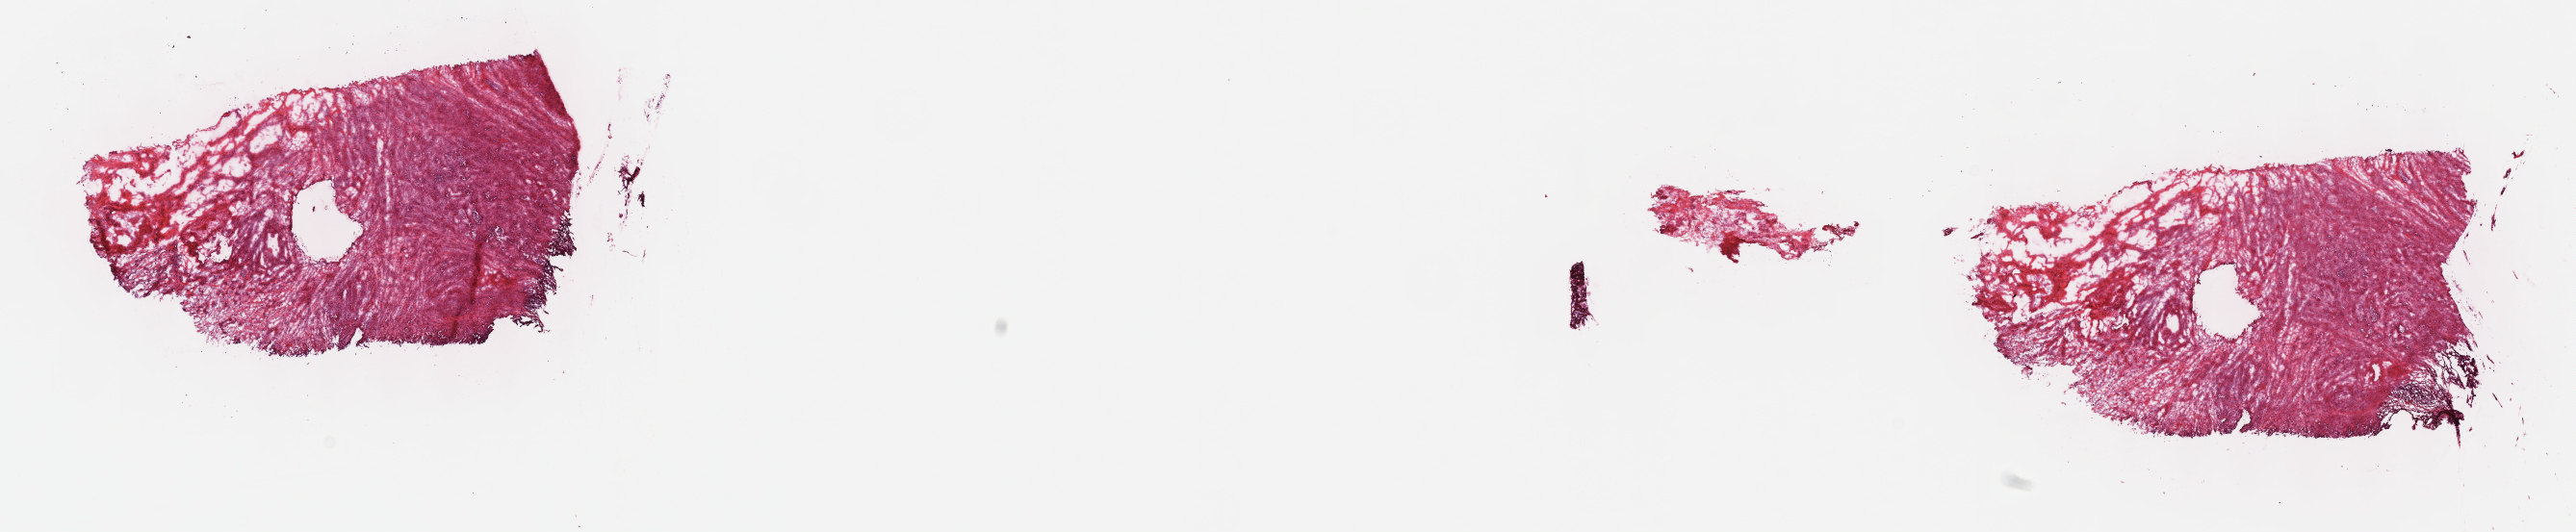
Digitized H&E tissue section (whole slide) — low-resolution overview of the scanned area, about 21.6 x 4.5 mm, frozen section from the top of the tissue portion, primary tumour sample from the stomach. Male, age 69 years at initial diagnosis. Histologic grade: G3 (poorly differentiated). Pathologist review of this section (percent, as recorded): tumour cells 70%, tumour nuclei 70%, normal cells 0%, stromal cells 20%, necrosis 10%. Inflammatory infiltration, as recorded: lymphocyte infiltration 40%, monocyte infiltration 20%, neutrophil infiltration 20%.
- AJCC pathologic stage: IIIB (7th edition)
- diagnosis: Adenocarcinoma, NOS (cardia, NOS)
- TNM: T3 N3 M0
- lymph nodes positive (case pathology): 12 of 12 examined